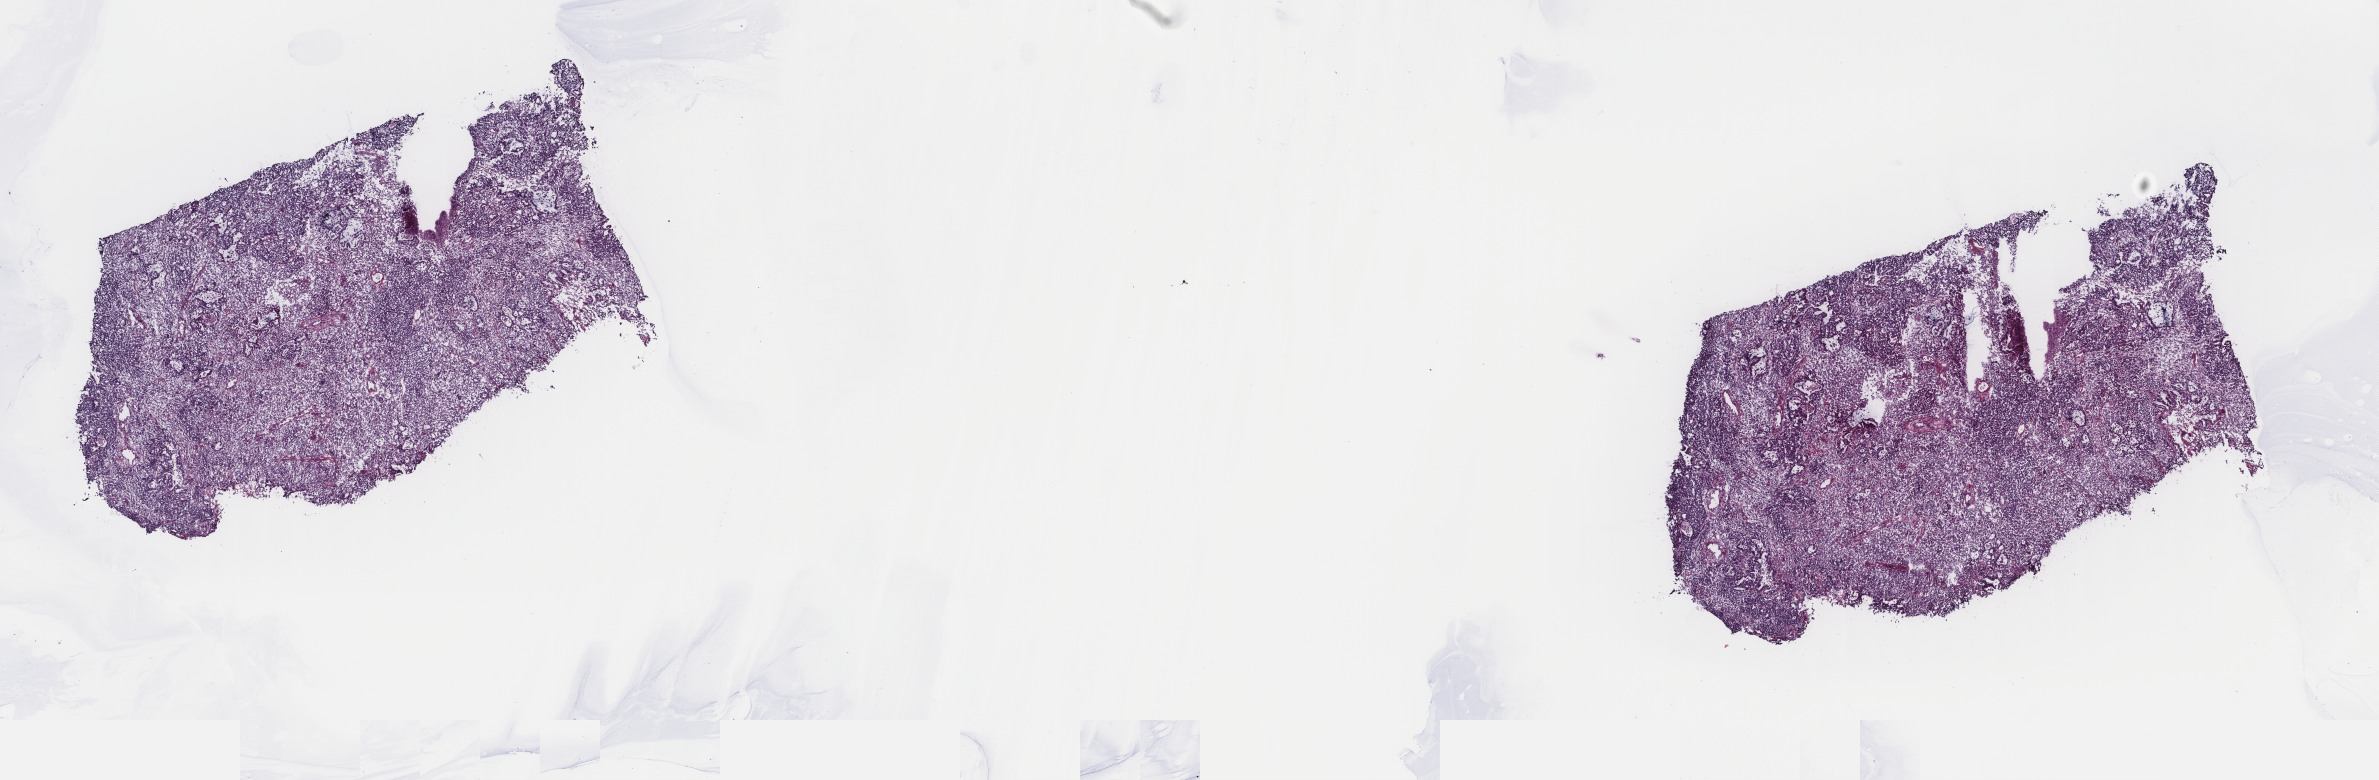
Digitized H&E tissue section (whole slide), shown as a low-resolution overview of the whole scanned area (about 18.9 x 6.2 mm, slide scanned at 40x), frozen section from the top of the tissue portion, uterus, primary tumour sample. Female patient; age at initial diagnosis 81 years. Slide review estimates, as recorded: tumour cells 90%, tumour nuclei 90%, normal cells 0%, stromal cells 10%, necrosis 0%. Inflammatory infiltration, as recorded: lymphocyte infiltration 0%, monocyte infiltration 0%, neutrophil infiltration 0%.
- FIGO stage: IIIA
- diagnosis: Mullerian mixed tumor (endometrium)